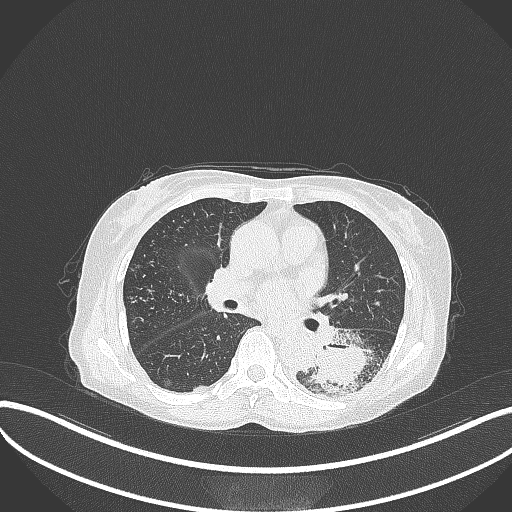
Chest CT, one axial slice. Slice 168 of 370 in the series (ordered by position). 120 kVp. Lung window (W 1500 / L -600 HU). 1 mm slice thickness. 512 × 512 image matrix. Patient: female, 78 years. From the clinical record (not read from this slice): clinical TNM (as recorded): T3 N0 M1.
Structures marked on this image (bounding box drawn by a radiologist):
- lung tumour (recorded histology: squamous cell carcinoma): bounding box <312,330,385,397> (left, top, right, bottom; pixels)